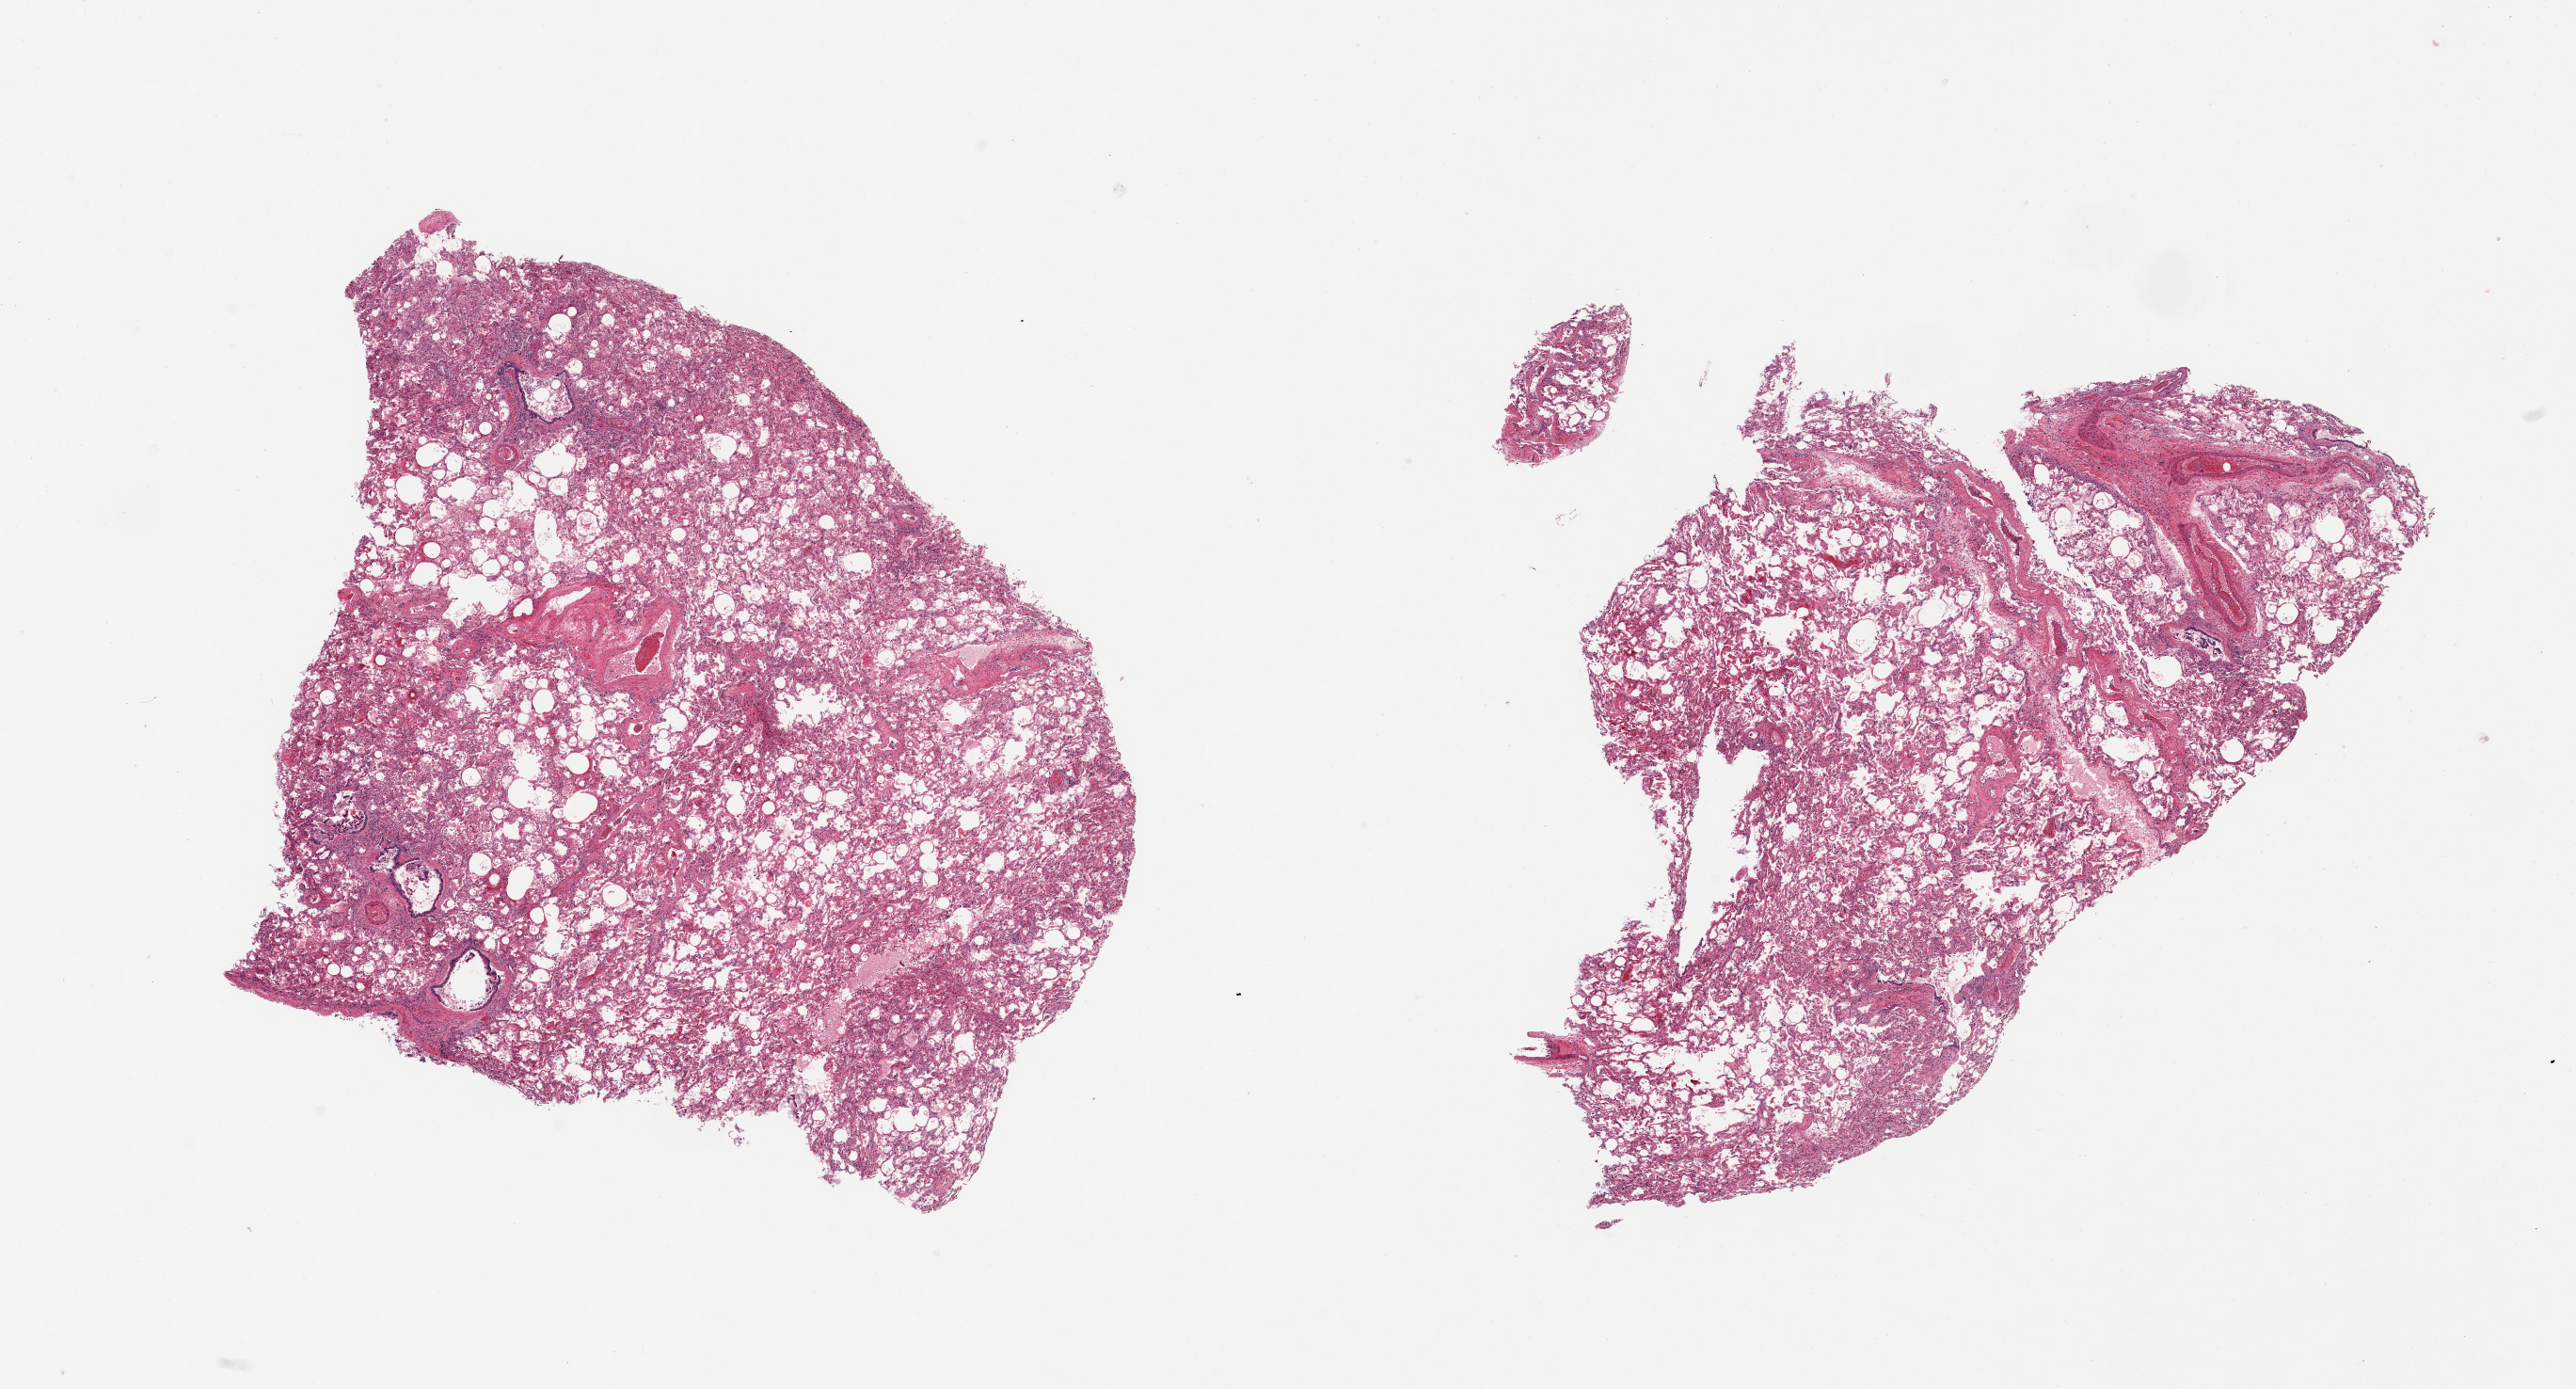
Digitized hematoxylin and eosin (H&E)-stained section — whole scanned area (about 21.7 x 11.7 mm, acquisition: 20x scan) shown as a low-resolution overview. PAXgene-fixed, paraffin-embedded tissue. Section of lung (target tissue). Tissue donor sample. Donor: female.
- pathologist's review note for this sample: 2 pieces, moderate congestion, acute pneumonia/pneumonitis/bronchitis